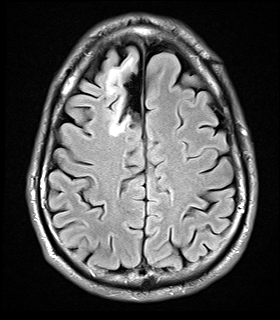
Brain MRI from a brain-tumour surgery series, one axial slice; position 9 of 32 along the scan axis; T2 FLAIR; 5 mm slice thickness; 280 × 320 image matrix, field of view 184 × 210 mm. Case-level facts recorded for this patient, not image findings: histopathology: Glial fibroma; tumour location: Right Frontal.
Outlined on this slice (manually delineated by an expert):
- tumour: box from (x=105, y=55) to (x=139, y=136) px